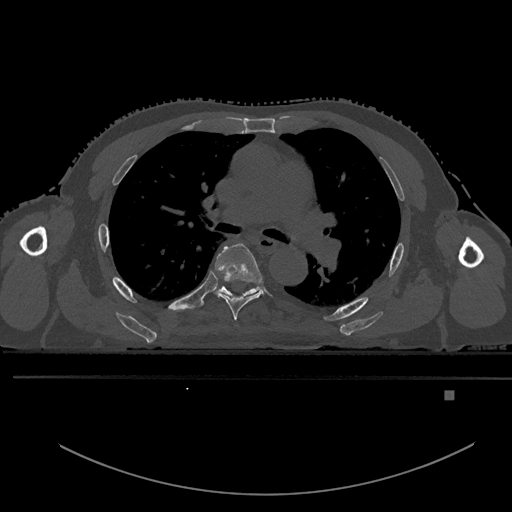
CT including the spine, one axial slice. Slice 342 of 969 in the series (ordered by position). Bone window (W 1800 / L 400 HU). 512 × 512 image matrix, field of view 456 × 456 mm. Male patient, age 82 years. From the clinical record (not read from this slice): primary cancer: prostate.
Structures marked on this image (semi-automatically segmented with operator editing):
- T5 vertebra: bounding box <214,243,264,320> (left, top, right, bottom; pixels)
- T6 vertebra: <198,286,261,307>